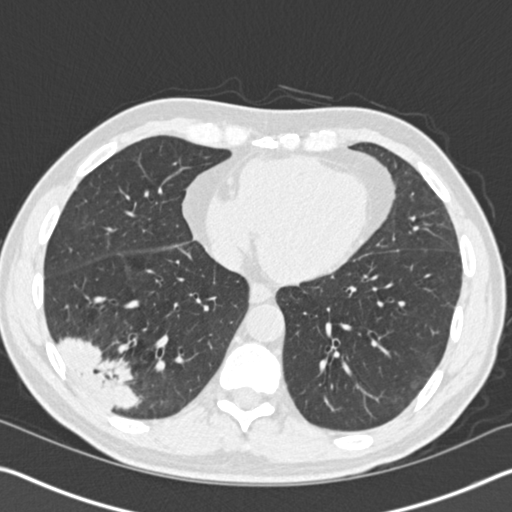
Low-dose screening chest CT, axial slice. Baseline screening round. Lung window (W 1500 / L -600 HU). 512 × 512 image matrix. Male, age 61 years at enrolment.
Expert reader's lesion annotation, bounding box (x1, y1, x2, y2) in pixels: (34, 307, 150, 420). Reader record for this screening exam (exam-level; its link to the box is not recorded): non-calcified nodule or mass ≥4 mm, right lower lobe, 52 × 36 mm, spiculated (stellate) margins, soft tissue attenuation.